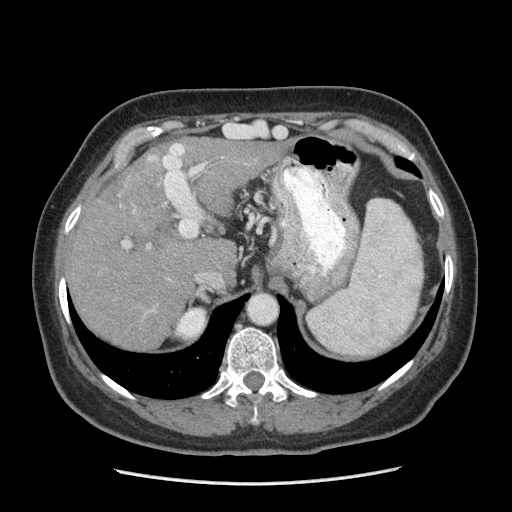
Contrast-enhanced abdominal CT (liver protocol), one axial slice; slice 159 of 185 in the series (ordered by position); 140 kVp; soft-tissue window (W 400 / L 40 HU); 512 × 512 image matrix, field of view 360 × 360 mm. From the clinical record (not read from this slice): diagnosis: hepatocellular carcinoma (patient treated with transarterial chemoembolisation; whether this scan precedes or follows treatment is not stated here); TNM stage (as recorded): Stage-I; Child-Pugh class: A.
Outlined on this slice (semi-automatic segmentation, software-assisted and operator-edited):
- abdominal aorta: bounding box [x1, y1, x2, y2] px = [250, 296, 275, 323]
- liver parenchyma outside the tumour (the mass and vessels are separate outlines, so this box may not span the whole liver): [66, 137, 272, 348]
- mass: [115, 161, 167, 230]
- liver vessels: [122, 143, 223, 275]